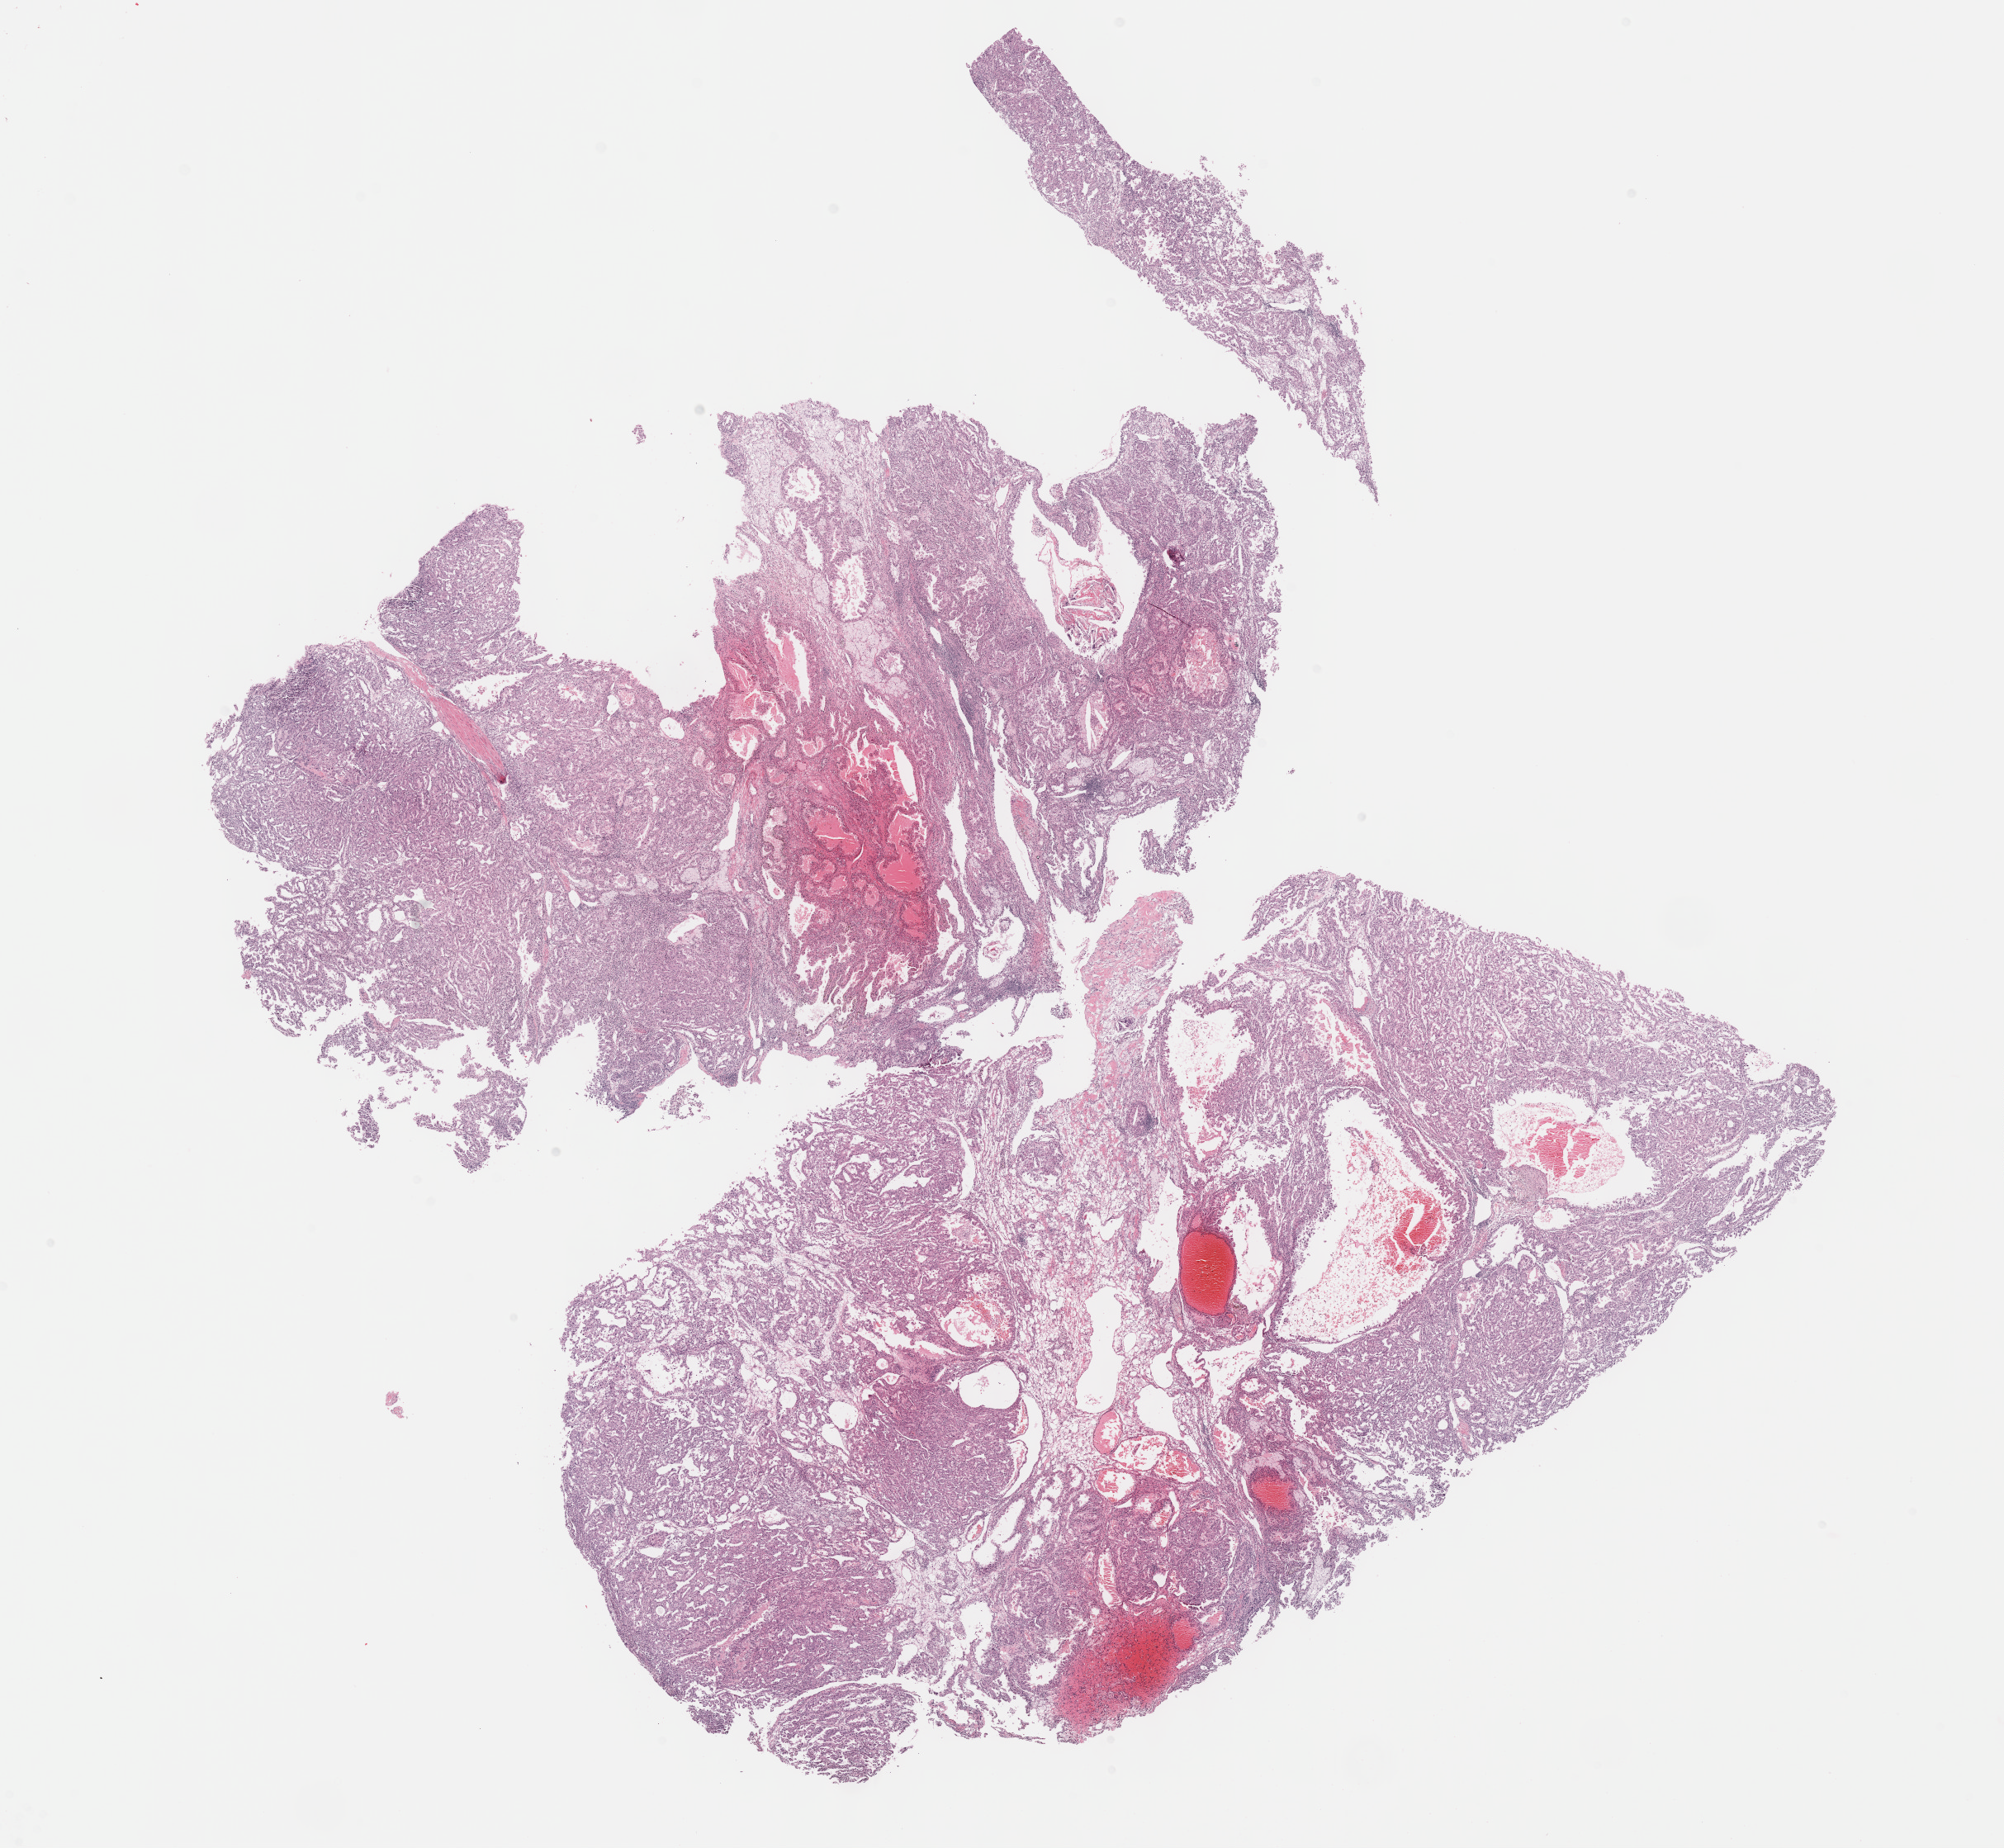
H&E whole-slide image — whole scanned area (about 19.6 x 18.1 mm) shown as a low-resolution overview, formalin-fixed paraffin-embedded (FFPE) diagnostic section, sample: primary tumour, kidney. Patient: male, age at initial diagnosis 48 years. Histologic grade: G3 (poorly differentiated).
AJCC pathologic stage: II (6th edition). Pathologic diagnosis: Clear cell adenocarcinoma, NOS. Lymph nodes positive (case pathology): 0 of 16 examined.